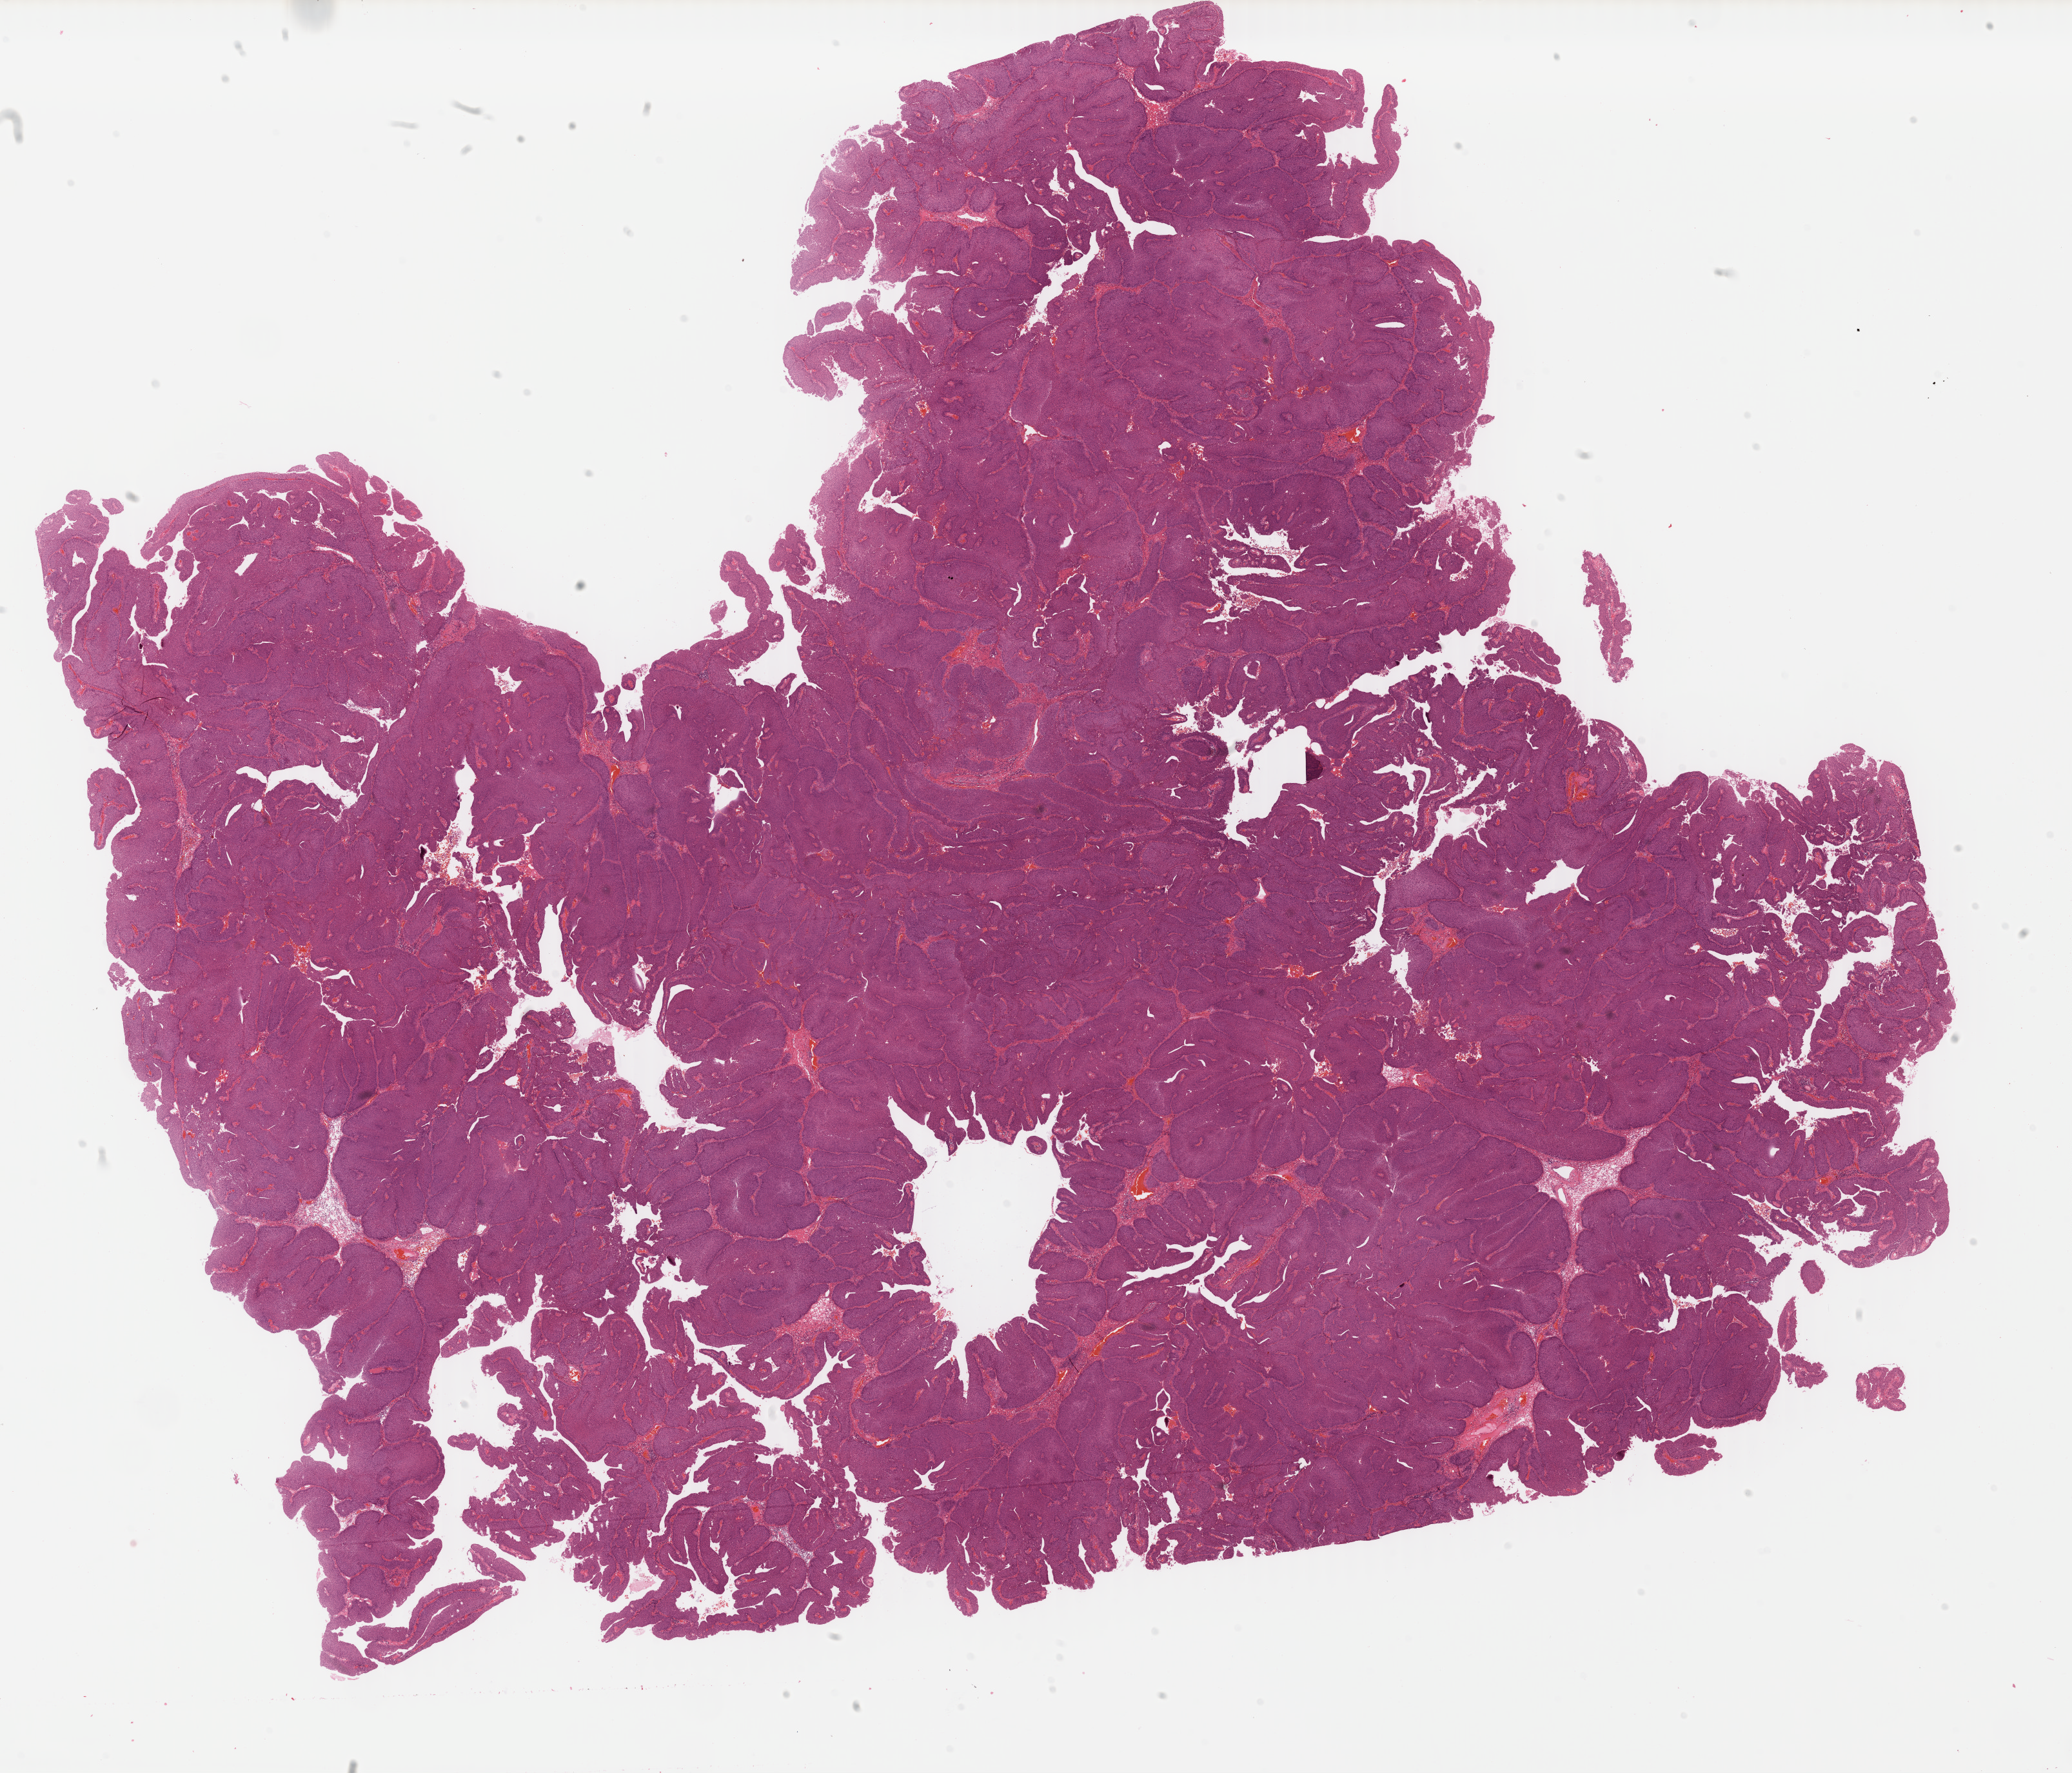
Hematoxylin and eosin (H&E) stained whole-slide image — shown as a low-resolution overview of the whole scanned area (about 25.3 x 21.6 mm); formalin-fixed paraffin-embedded (FFPE) diagnostic section; primary tumour sample from the bladder. Patient: male, age at initial diagnosis 55 years. Histologic grade: low grade.
- histologic diagnosis: Transitional cell carcinoma
- AJCC pathologic stage: III